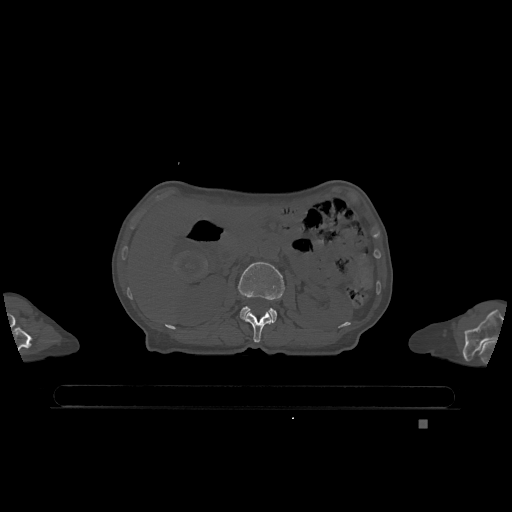
CT including the spine, one axial slice; position 444 of 1317 along the scan axis; bone window (W 1800 / L 400 HU); 512 × 512 image matrix, field of view 500 × 500 mm. Female patient, age 74 years. Case-level facts recorded for this patient, not image findings: primary cancer: lung.
Outlined on this slice (semi-automatic segmentation, software-assisted and operator-edited):
- L1 vertebra: bounding box <244,312,272,343> (left, top, right, bottom; pixels)
- L2 vertebra: <238,262,285,323>